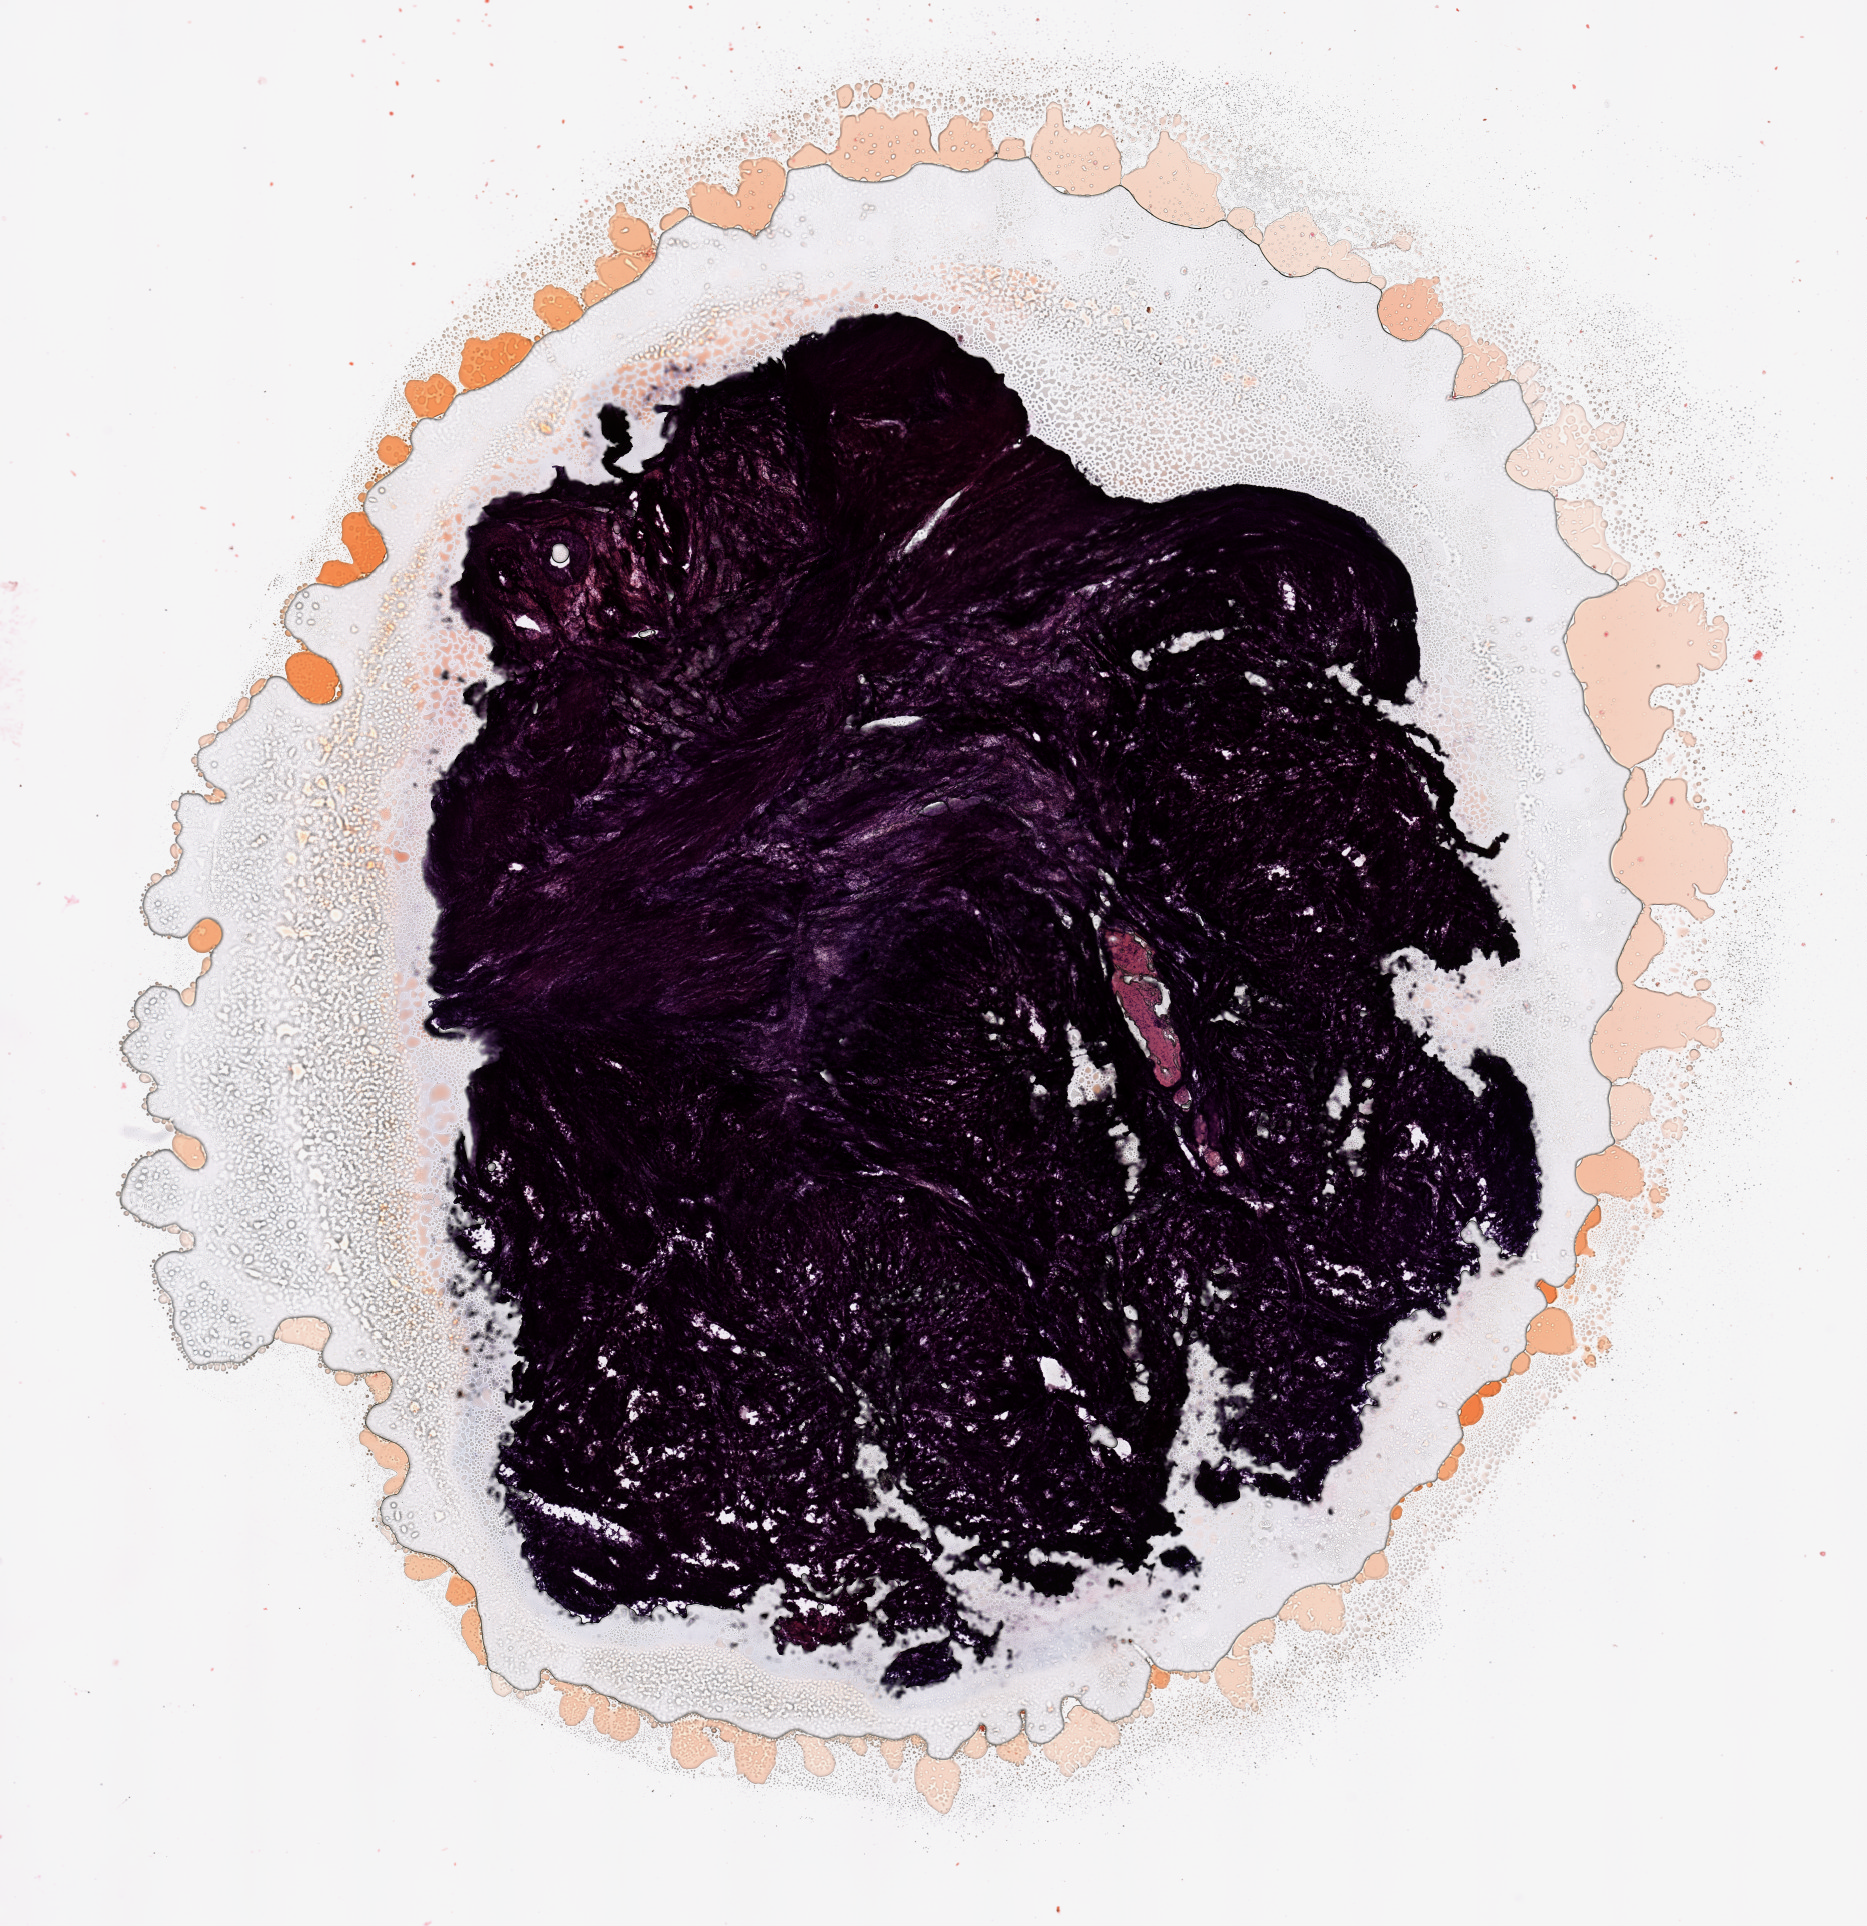
Whole-slide histology image, Hematoxylin and eosin (H&E) stained, a low-resolution overview of the entire scanned area, about 14.8 x 15.2 mm (acquisition: 20x scan); uterus, tumour tissue. Patient: female, age 75 years. Histologic grade: G3 (poorly differentiated).
• AJCC pathologic stage: I
• diagnosis: Endometrioid adenocarcinoma, NOS